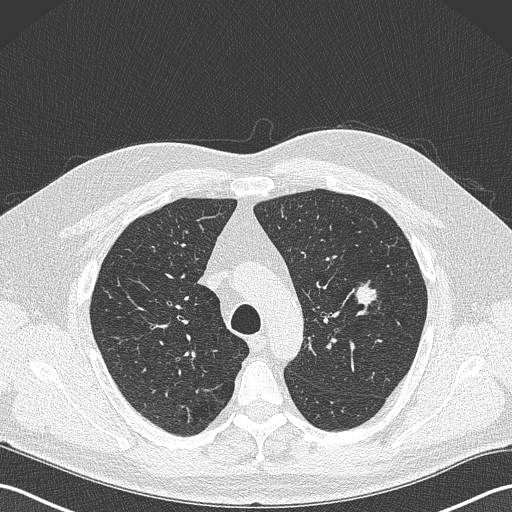
Low-dose screening chest CT, axial slice, baseline screening round, lung window (W 1500 / L -600 HU), 1 mm slice thickness, lung (sharp) reconstruction kernel (B50f), 120 kVp, slice 93 of 343 in the series, 512 × 512 image matrix. Male, age 61 years at enrolment.
Expert-annotated lung lesion, bounding box <347,280,385,314> (left, top, right, bottom; pixels). The screening reader recorded 2 non-calcified nodules or masses ≥4 mm on this exam (left upper lobe, lingula); which of them this box marks is not recorded. Official screen result: positive, change unspecified: nodule(s) >= 4 mm or enlarging nodule(s), mass(es), or other non-specific abnormalities suspicious for lung cancer. Participant outcome: lung cancer diagnosed 160 days after this screen — adenocarcinoma, NOS, left upper lobe, poorly differentiated (G3), stage IA (AJCC 6th edition), 28 mm at pathology.